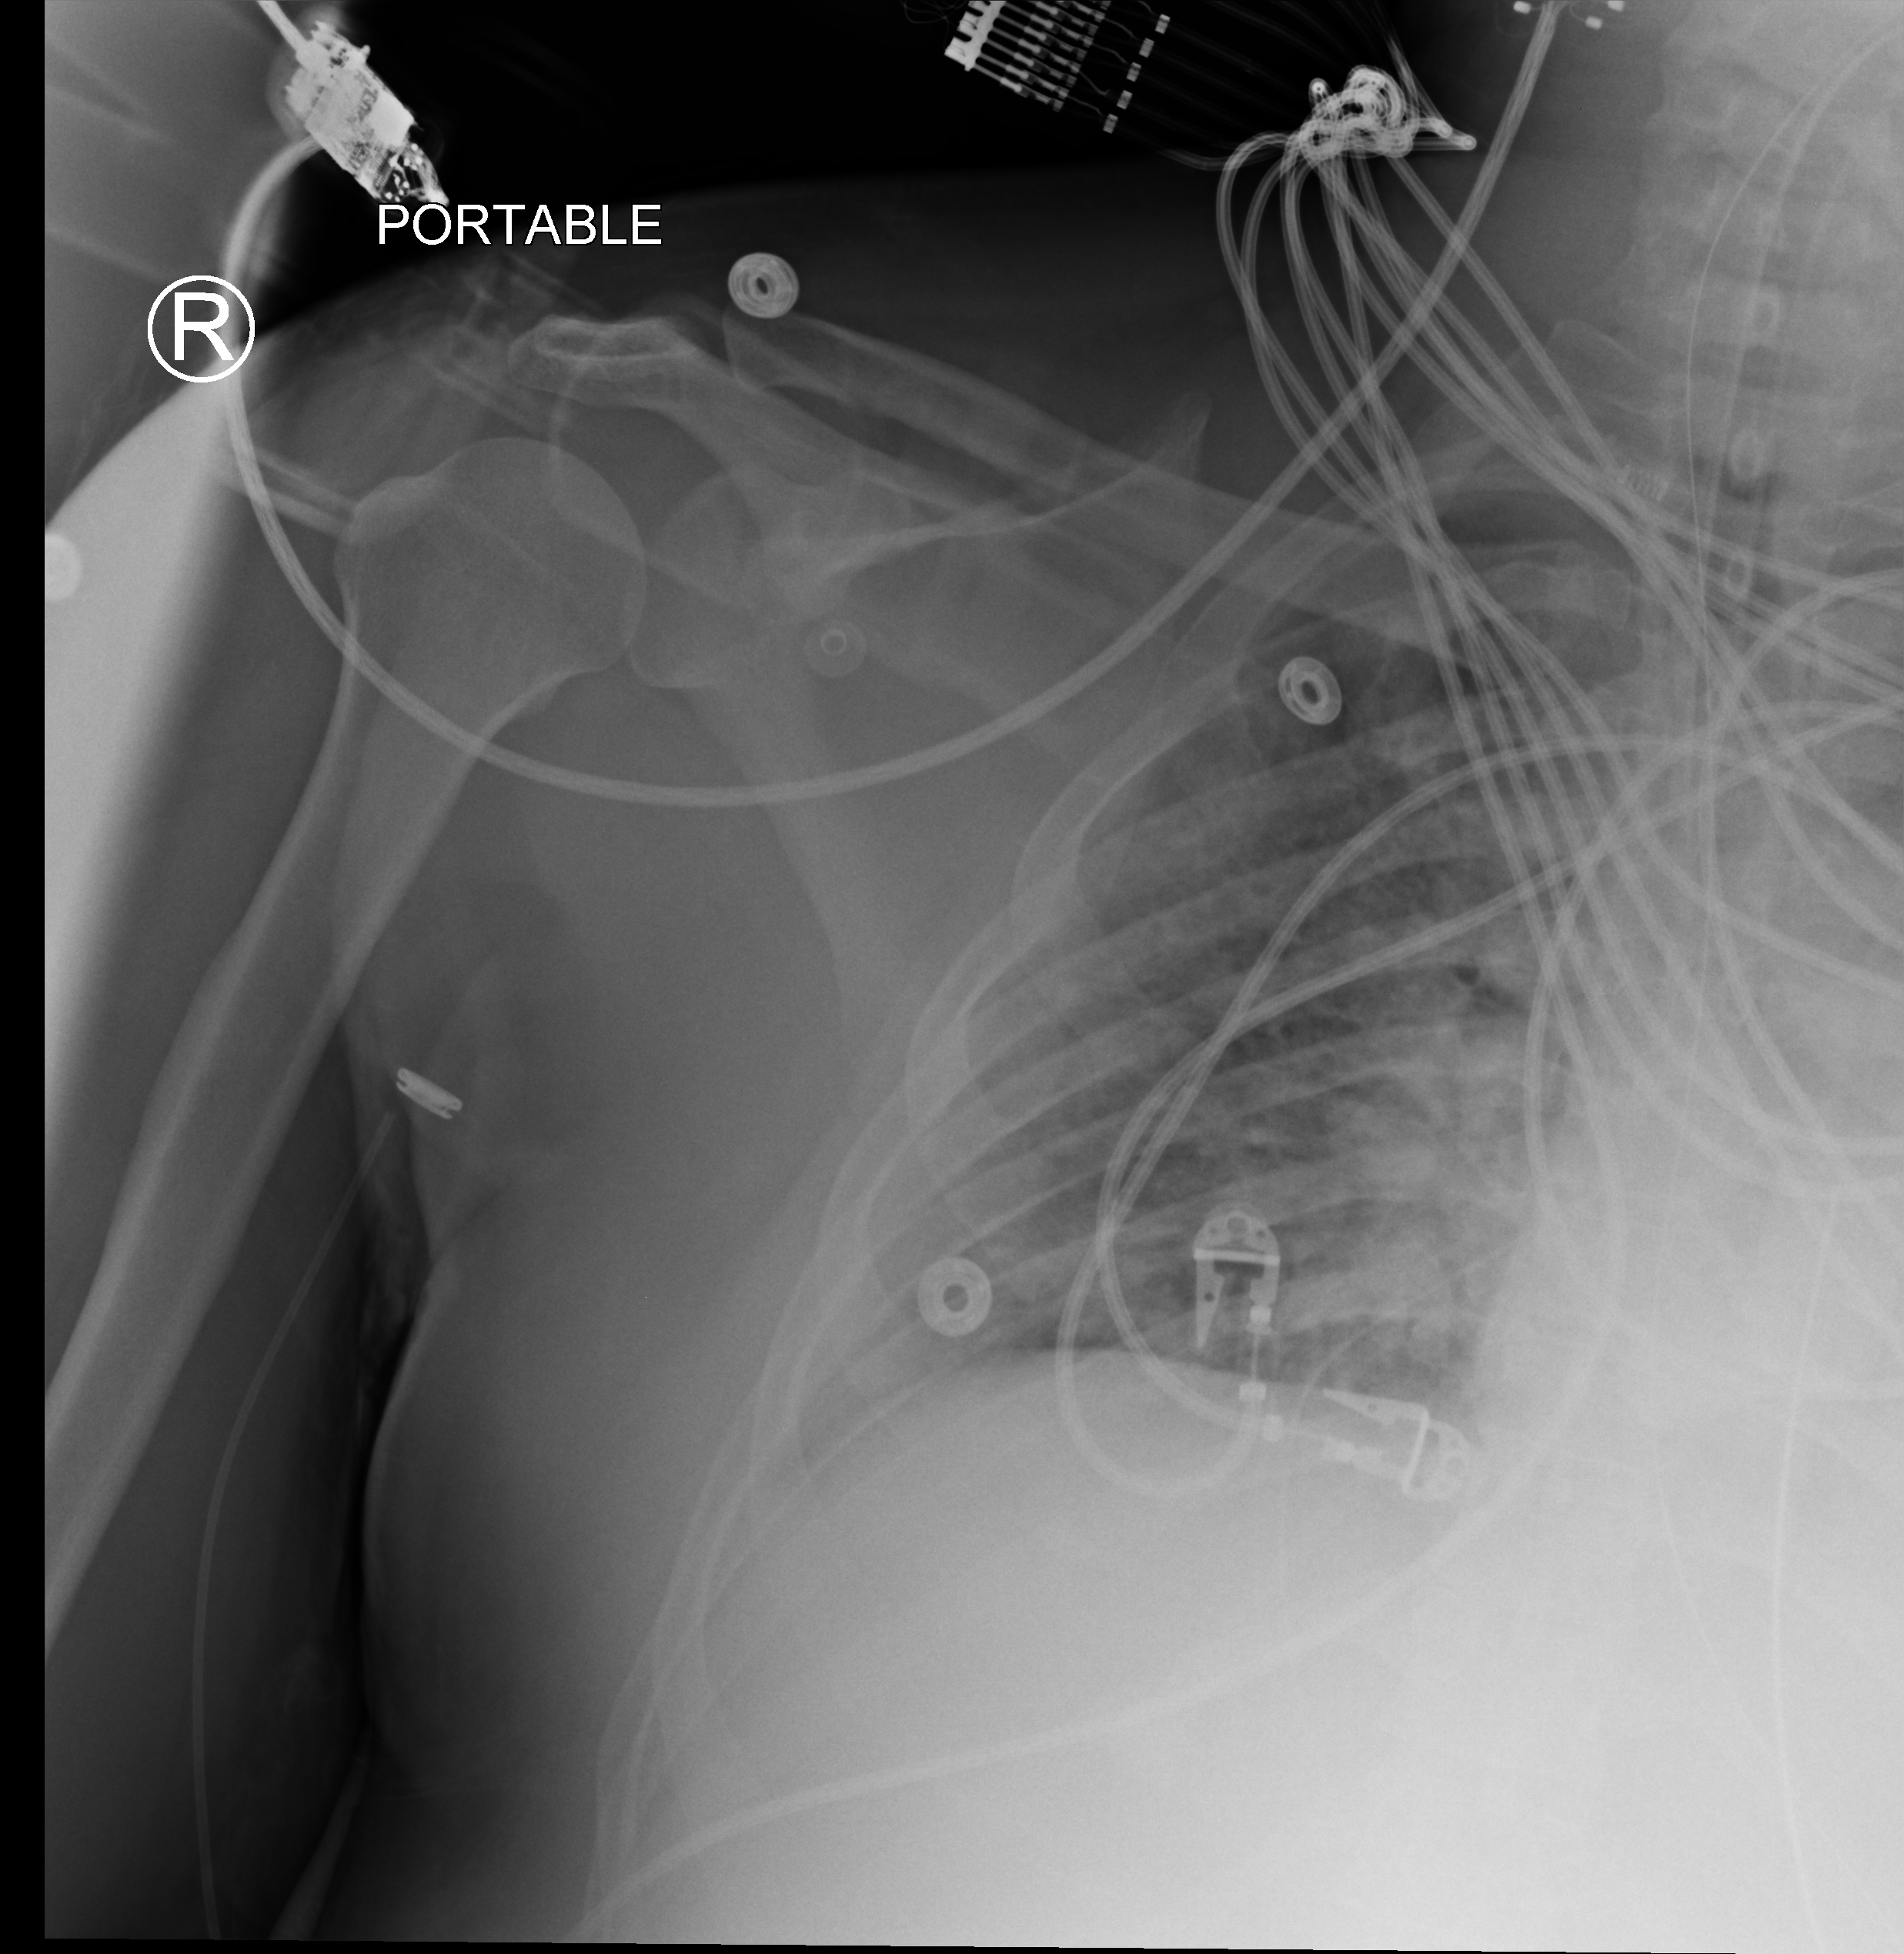
Chest X-ray (portable), anteroposterior (AP) projection. Patient hospitalised with COVID-19, aged 18–59 years.
Admission-level facts for this patient (not findings on this image; timing relative to this image not recorded):
- length of hospital stay: 19 days